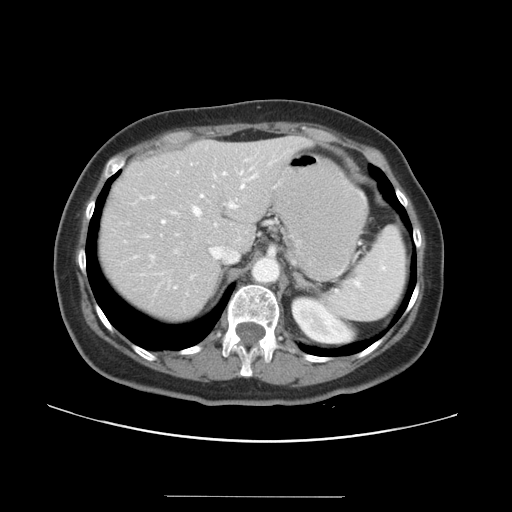
Contrast-enhanced abdominal CT, one axial slice. Reconstruction kernel STANDARD. 120 kVp. Intravenous contrast given. Soft-tissue window (W 400 / L 40 HU). 512 × 512 image matrix, field of view 382 × 382 mm. Female patient, age 69 years. From the clinical record (not read from this slice): diagnosis: colorectal cancer liver metastases, imaged before liver resection; multiple liver metastases: yes; largest metastasis: 1.4 cm; disease in both lobes: yes.
Outlined on this slice (expert manual segmentation):
- hepatic veins: box from (x=143, y=168) to (x=256, y=274) px
- liver: (x=99, y=137)–(x=308, y=320)
- planned liver remnant (the part of the liver to remain after resection): (x=99, y=137)–(x=308, y=320)
- portal vein (with intrahepatic branches): (x=151, y=173)–(x=225, y=259)